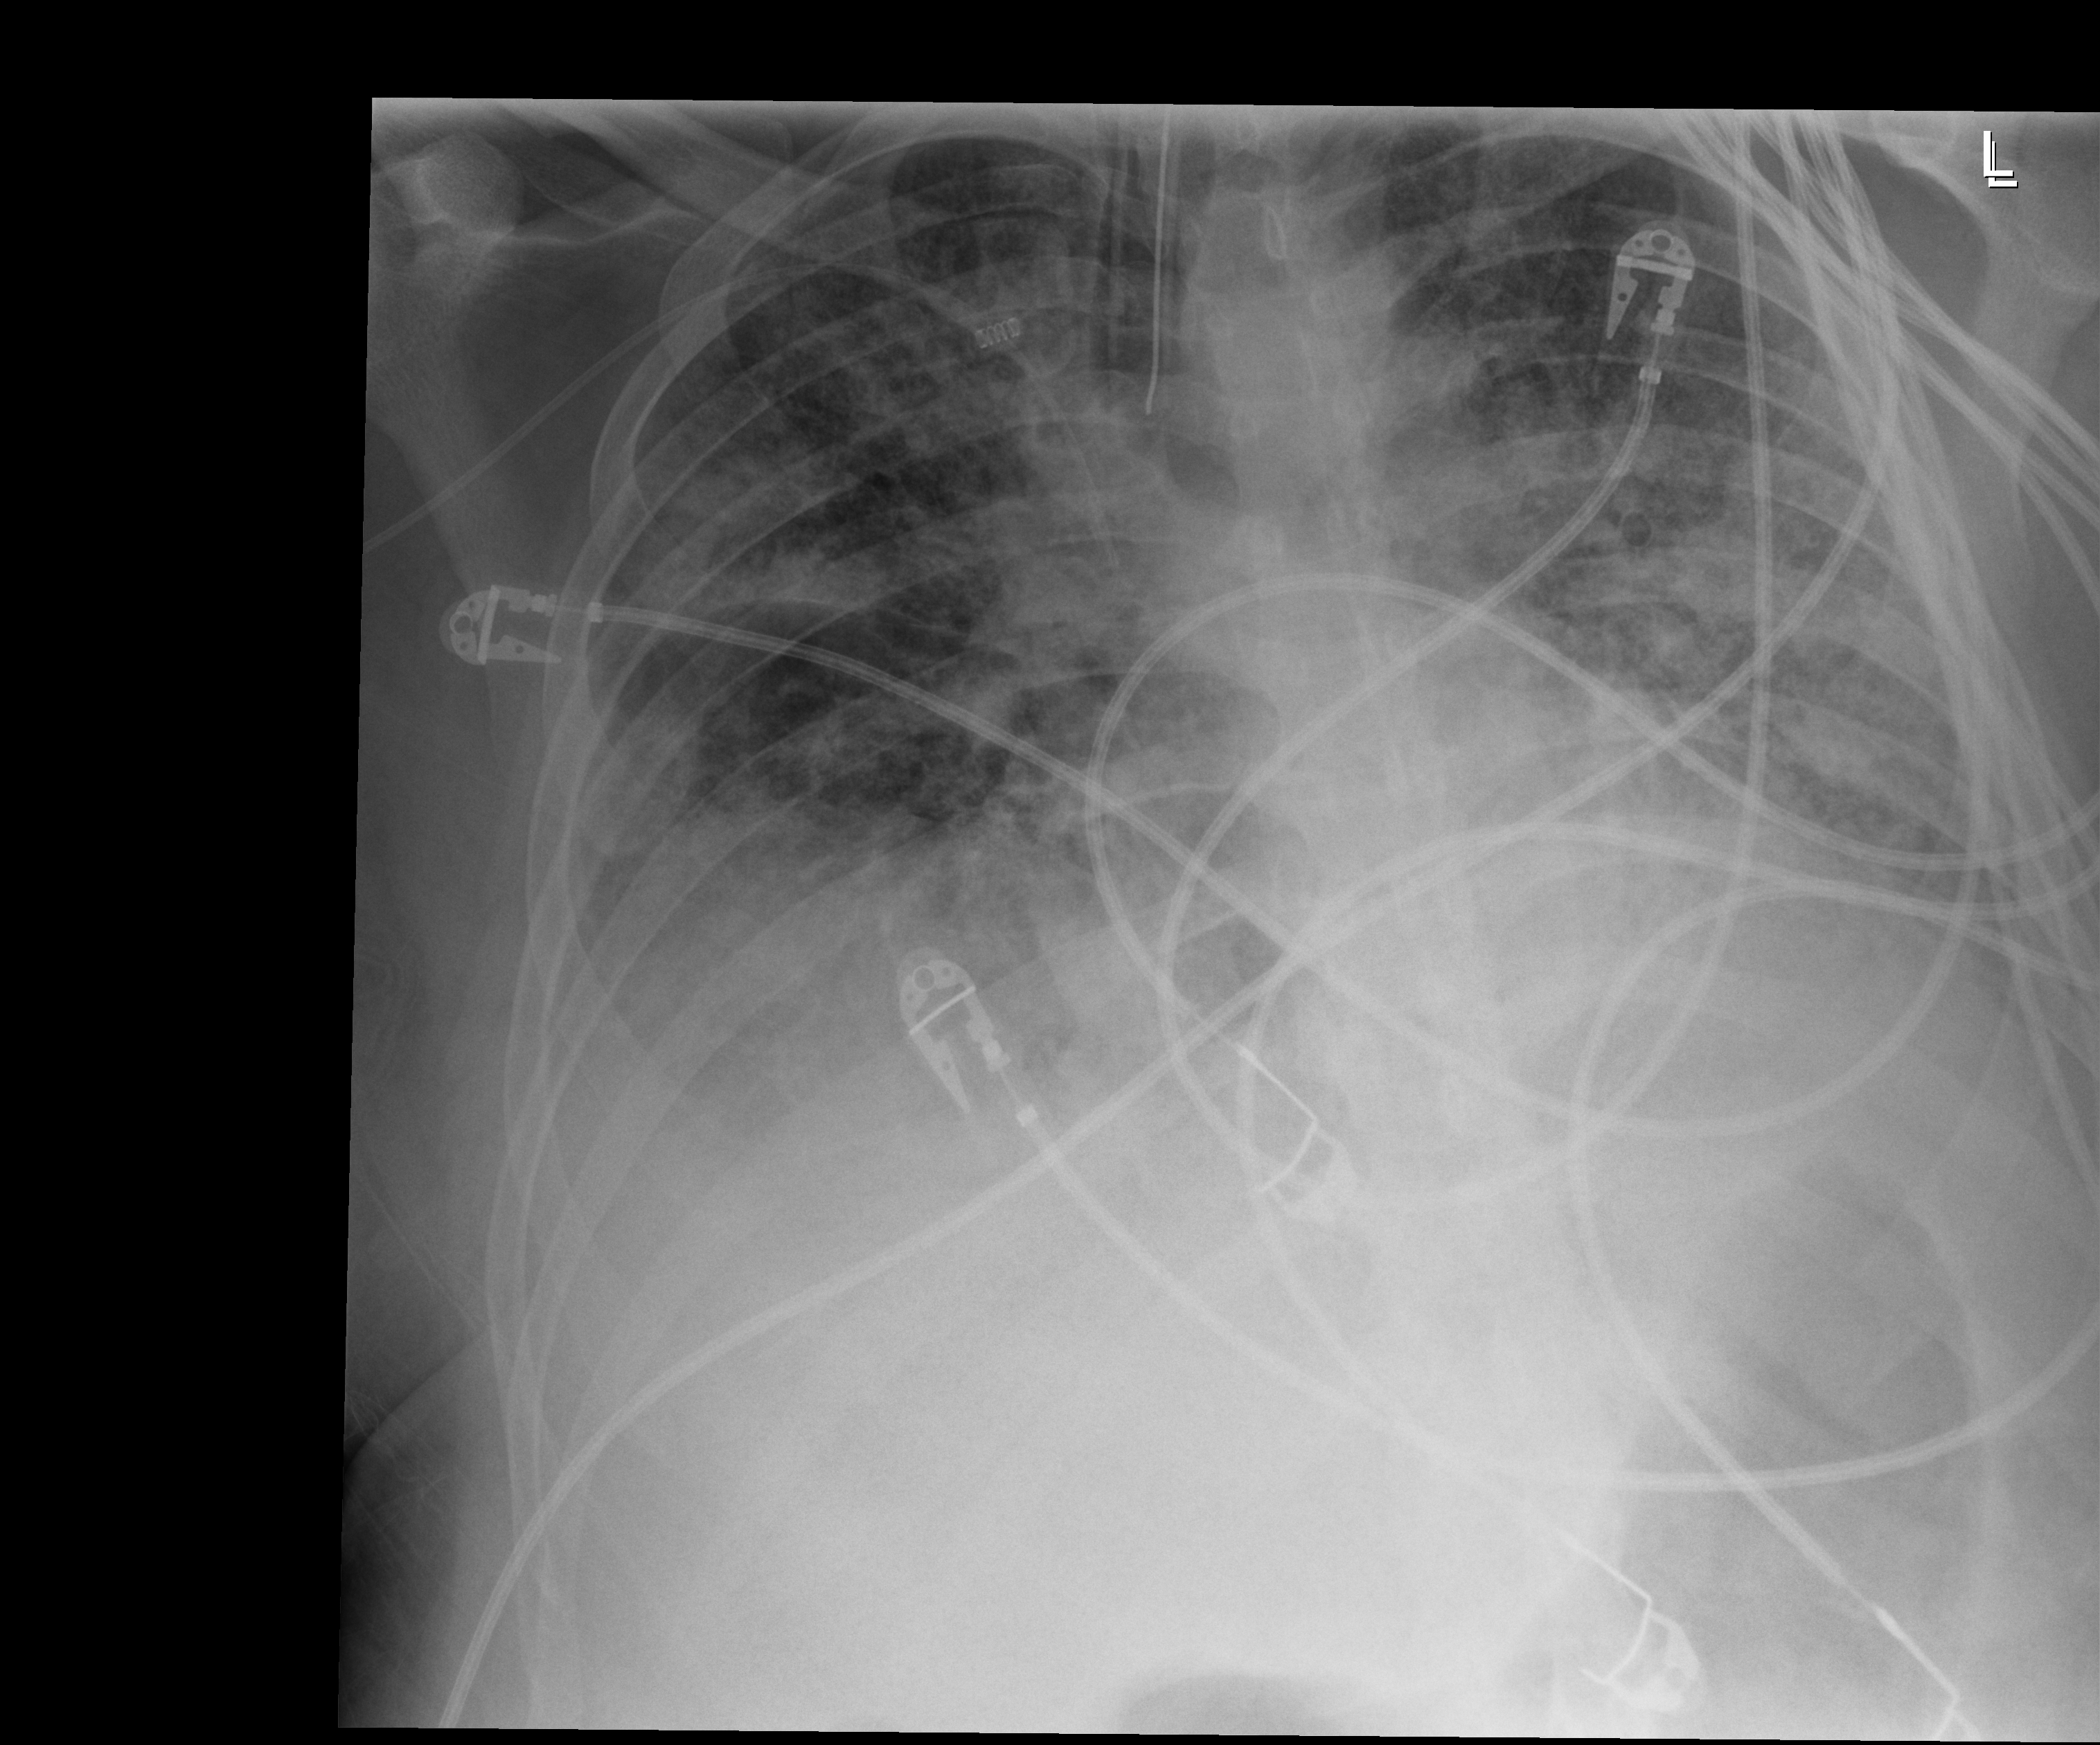
Chest X-ray (portable), anteroposterior (AP) projection. Patient hospitalised with COVID-19; male, aged 18–59 years.
Admission-level facts for this patient (not findings on this image; timing relative to this image not recorded): admitted to intensive care during this hospital stay: yes; length of hospital stay: 96 days; mechanically ventilated during this hospital stay: yes.